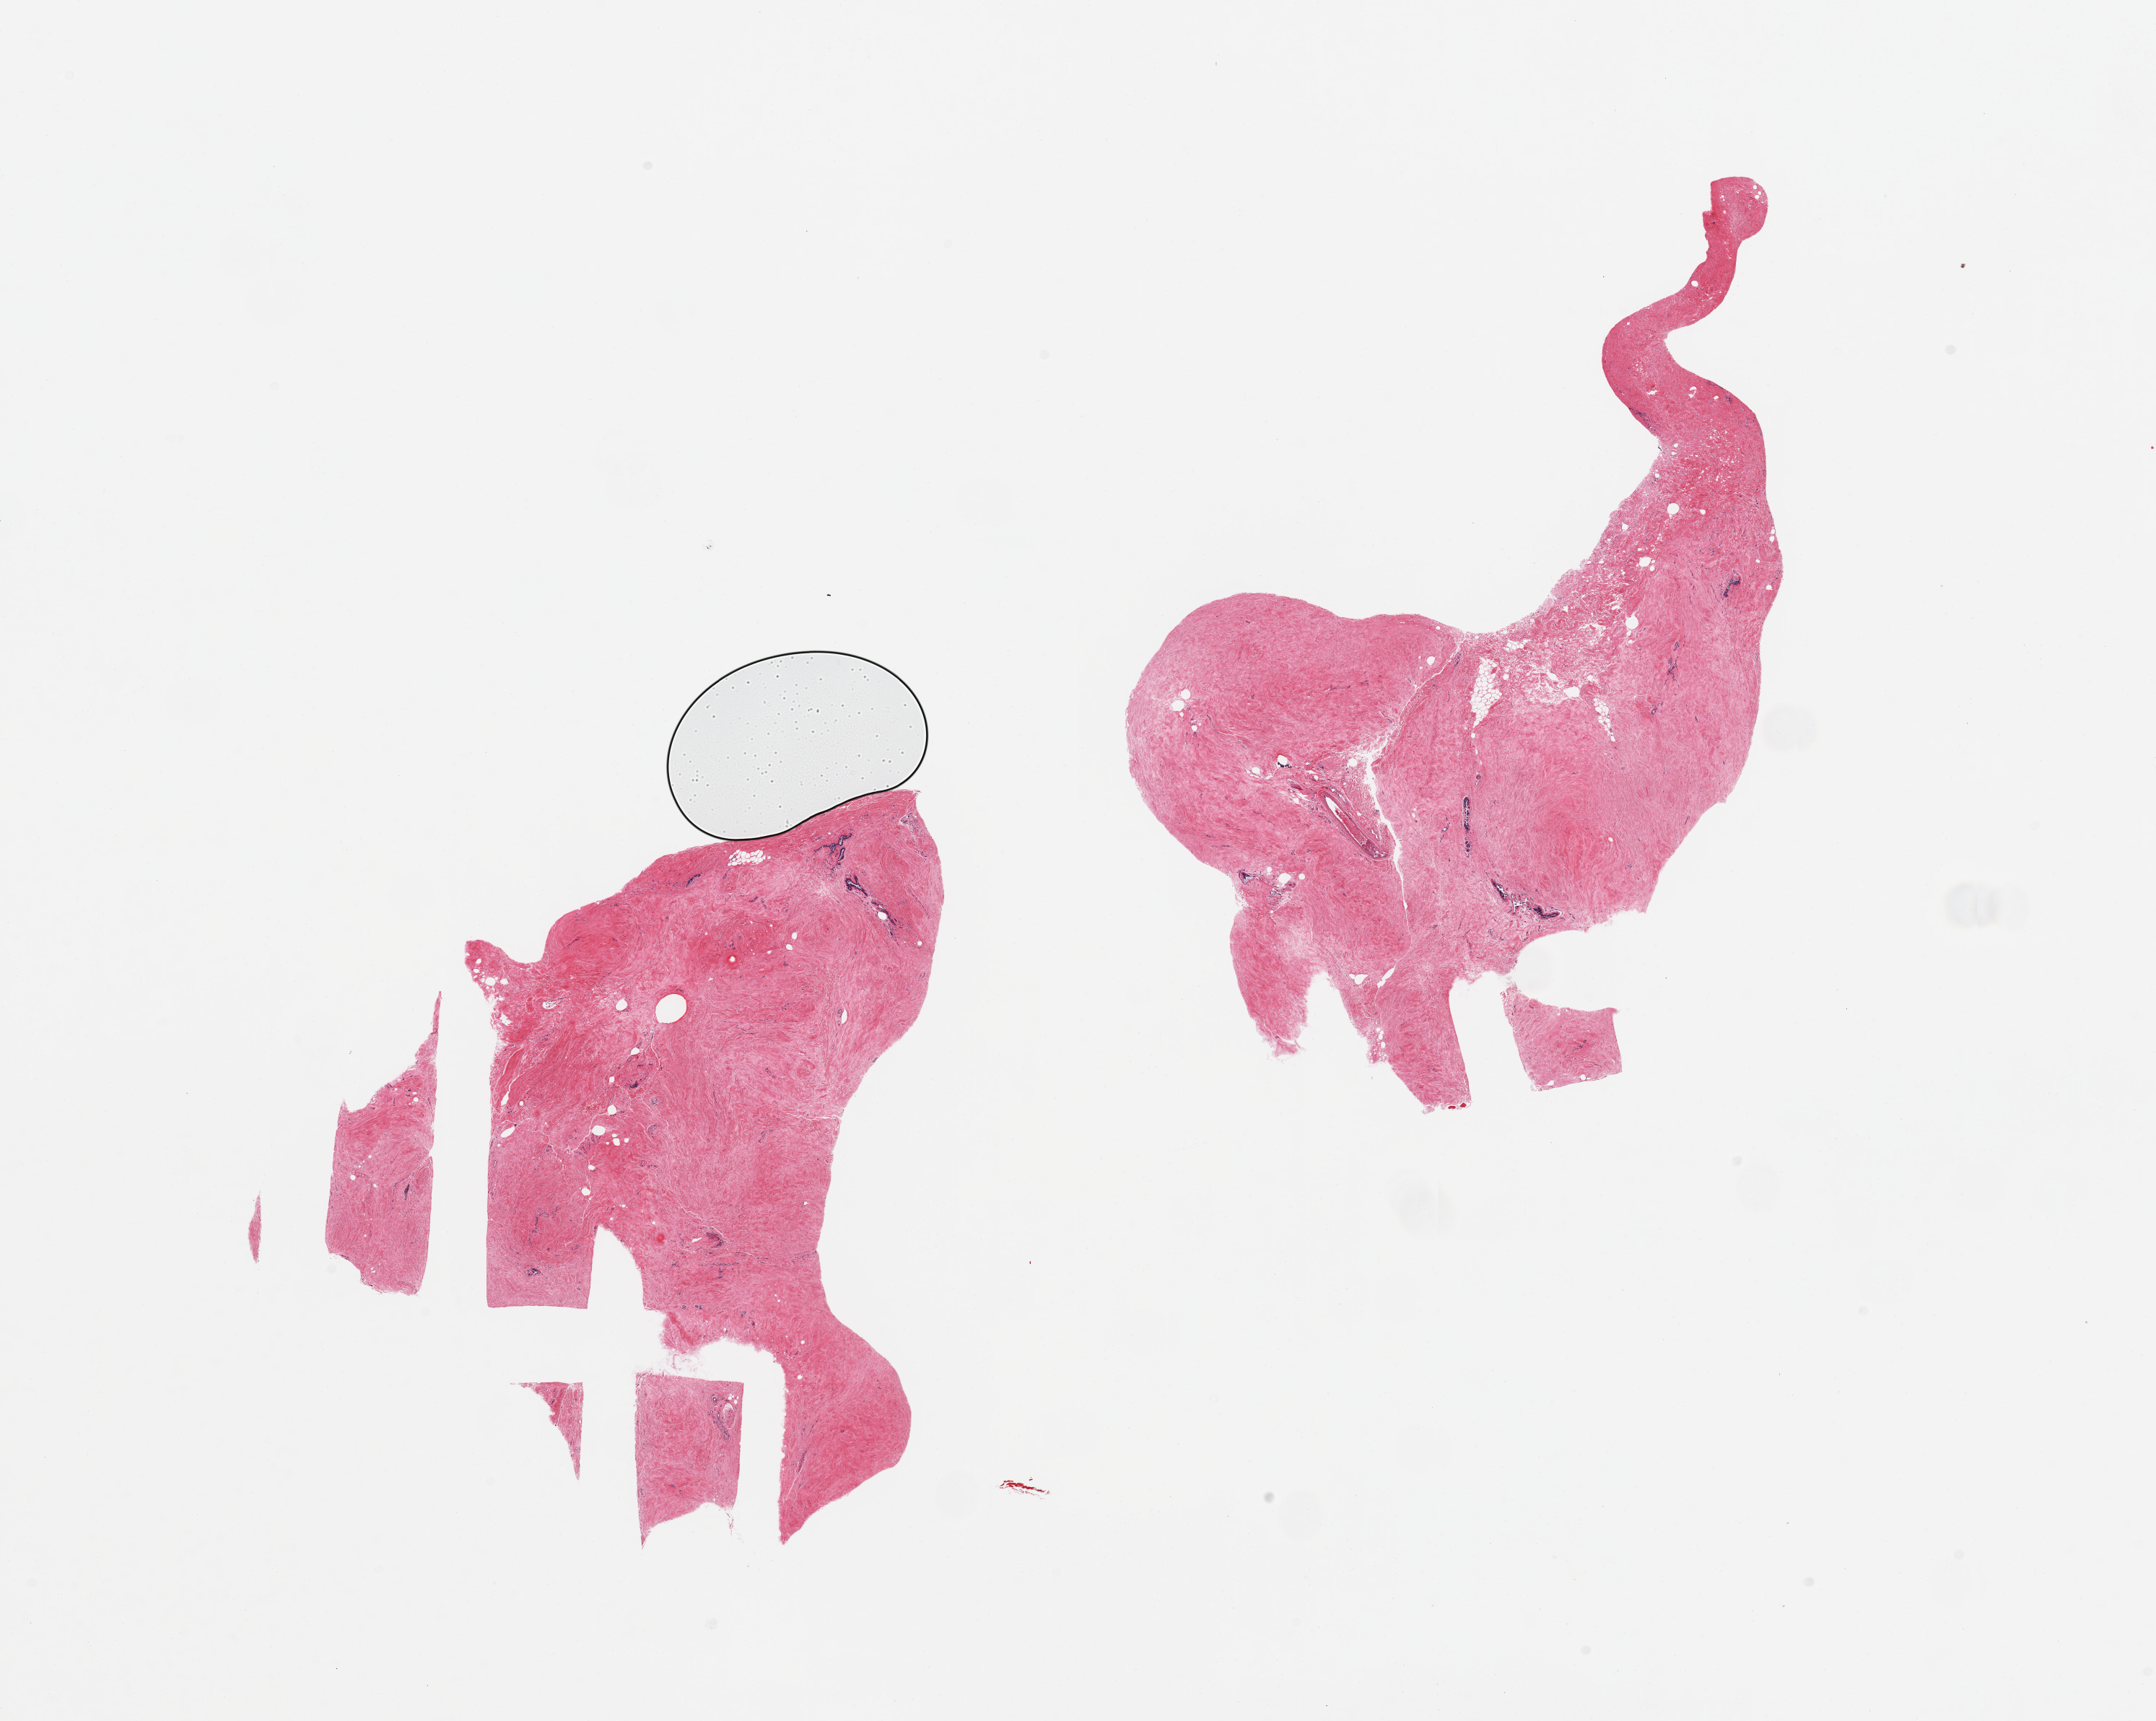
Digitized haematoxylin and eosin-stained section, brightfield — whole scanned area (about 23.6 x 18.9 mm) shown as a low-resolution overview. PAXgene-fixed paraffin-embedded (PFPE) section. Section of breast (target tissue). Tissue donor sample. Donor: male.
Pathologist's review note for this sample: 2 pieces; ductal structures embedded in dense fibrous stroma; minimal fat.